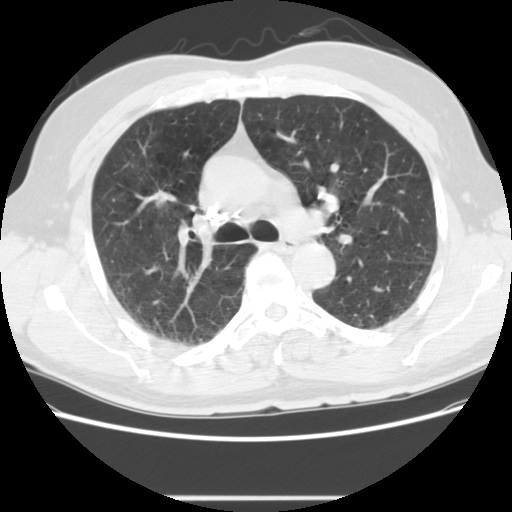
Low-dose screening chest CT, one axial slice. Position 89 of 139 along the scan axis. Reconstruction kernel STANDARD. 120 kVp. Lung window (W 1500 / L -600 HU). 2.5 mm slice thickness. 512 × 512 image matrix, field of view 360 × 360 mm.
Outlined on this slice (outlined manually by an expert reader):
- lesion 1 (tumor, upper lobe of right lung): bounding box <153,190,177,207> (left, top, right, bottom; pixels)